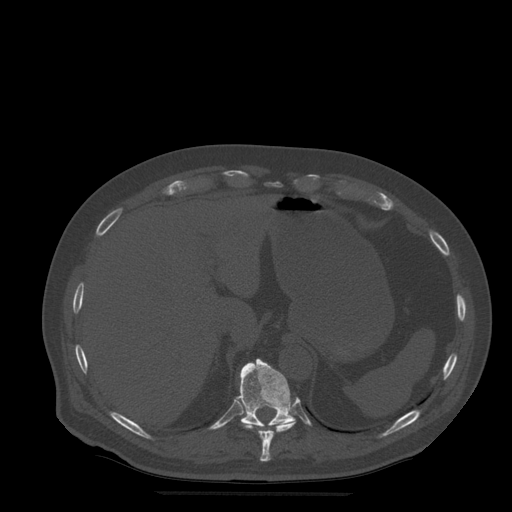
CT including the spine, one axial slice. Position 255 of 522 along the scan axis. Bone window (W 1800 / L 400 HU). 1.25 mm slice thickness. 512 × 512 image matrix, field of view 420 × 420 mm. Patient age 72 years. Case-level facts recorded for this patient, not image findings: primary cancer: prostate.
Outlined on this slice (semi-automatic segmentation, software-assisted and operator-edited):
- T10 vertebra: bounding box [x1, y1, x2, y2] px = [241, 421, 296, 462]
- T11 vertebra: [238, 359, 296, 428]